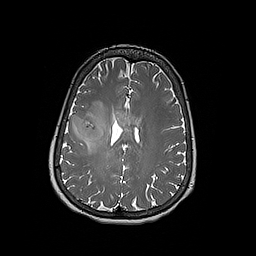
Brain MRI from a brain-tumour surgery series, one axial slice. Slice 77 of 192 in the series (ordered by position). 256 × 256 image matrix, field of view 250 × 250 mm. Case-level facts recorded for this patient, not image findings: histopathology: Oligodendroglioma; WHO grade: 3; IDH mutation: yes; tumour location: Right Frontal.
Structures marked on this image (outlined manually by an expert reader):
- tumour: bounding box [x1, y1, x2, y2] px = [70, 115, 104, 147]